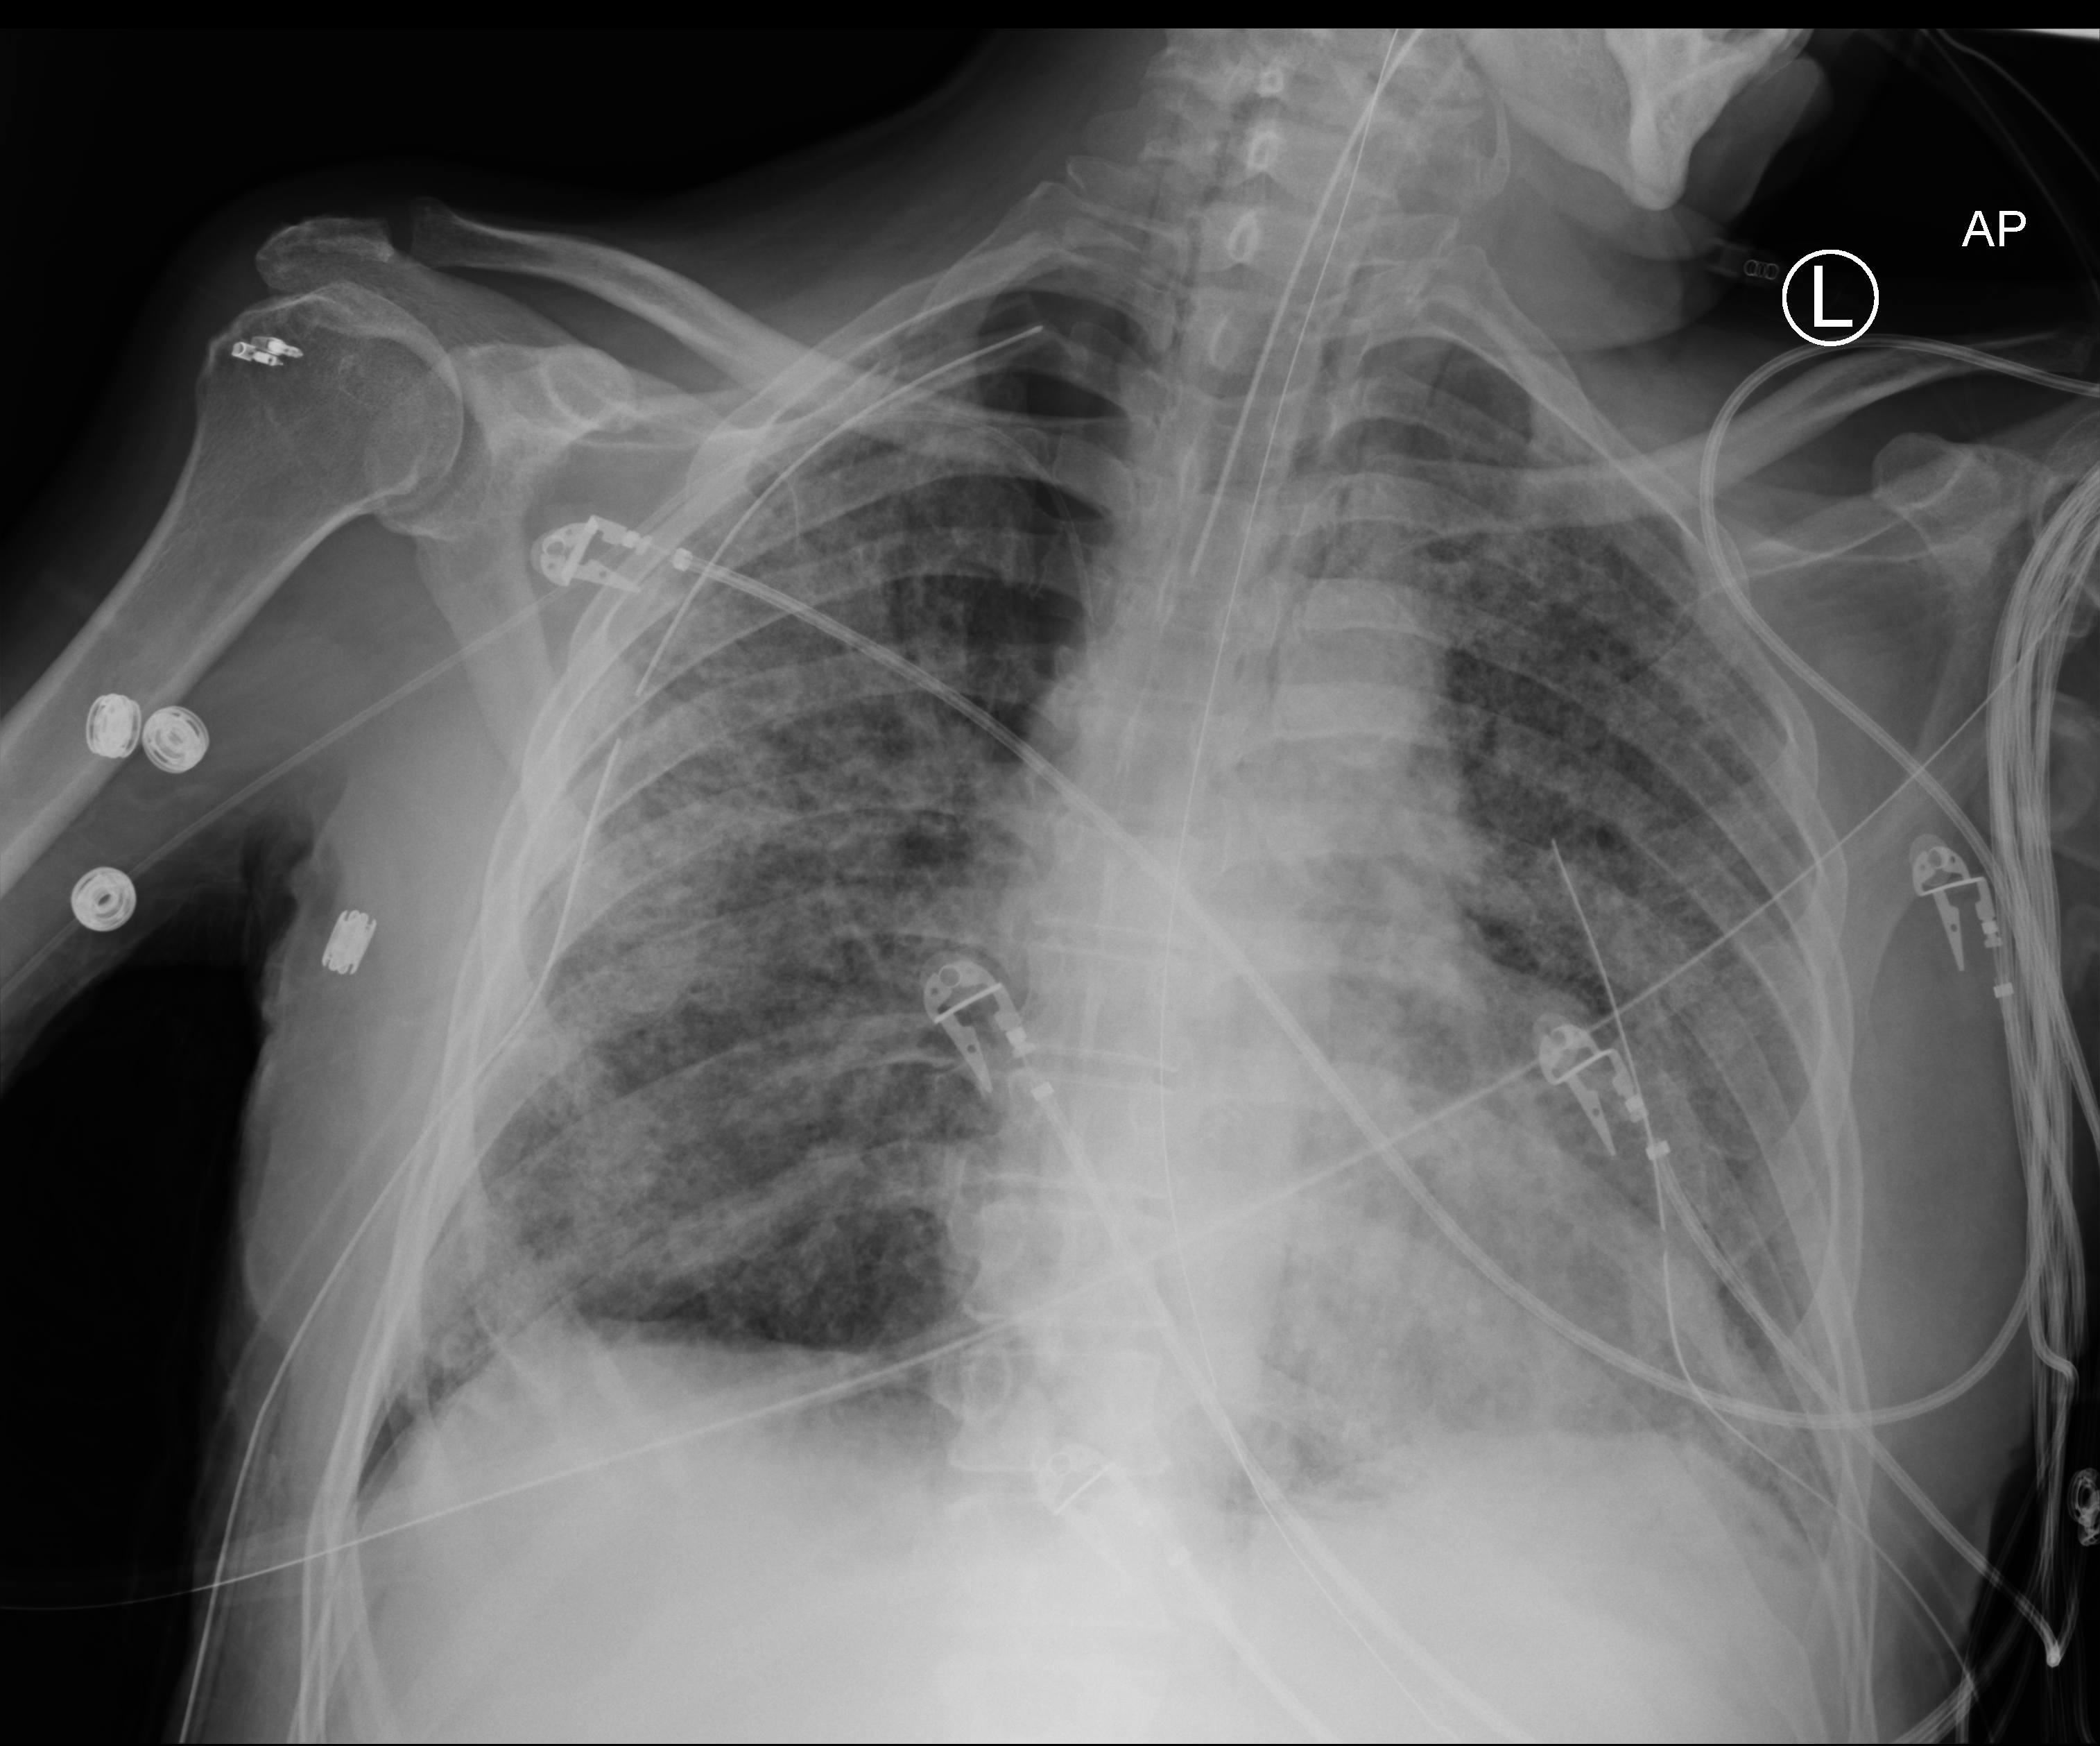
Portable chest radiograph; anteroposterior (AP) projection. Male patient hospitalised with COVID-19, age 60–74 years.
Admission-level facts for this patient (not findings on this image; timing relative to this image not recorded): other chronic lung disease (admission record): yes.